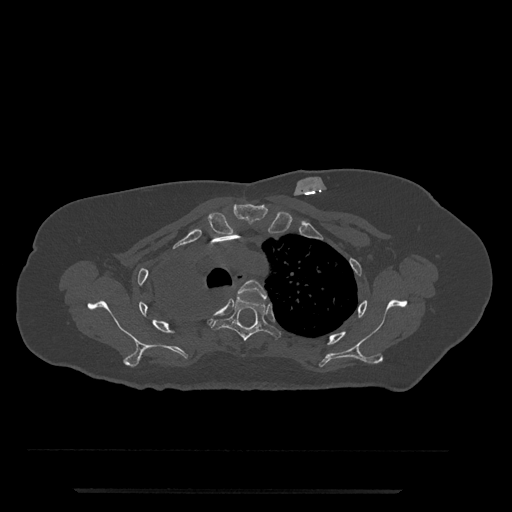
CT including the spine, one axial slice. Position 598 of 797 along the scan axis. Reconstruction kernel Br40s/3. Bone window (W 1800 / L 400 HU). 0.5 mm slice thickness. 512 × 512 image matrix, field of view 440 × 440 mm. Patient: female, 51 years. Case-level facts recorded for this patient, not image findings: primary cancer: neuro; vertebrae with lytic lesions (as recorded): T8.
Outlined on this slice (semi-automatically segmented with operator editing):
- T3 vertebra: bounding box [x1, y1, x2, y2] px = [238, 280, 267, 299]
- T4 vertebra: [210, 297, 281, 341]